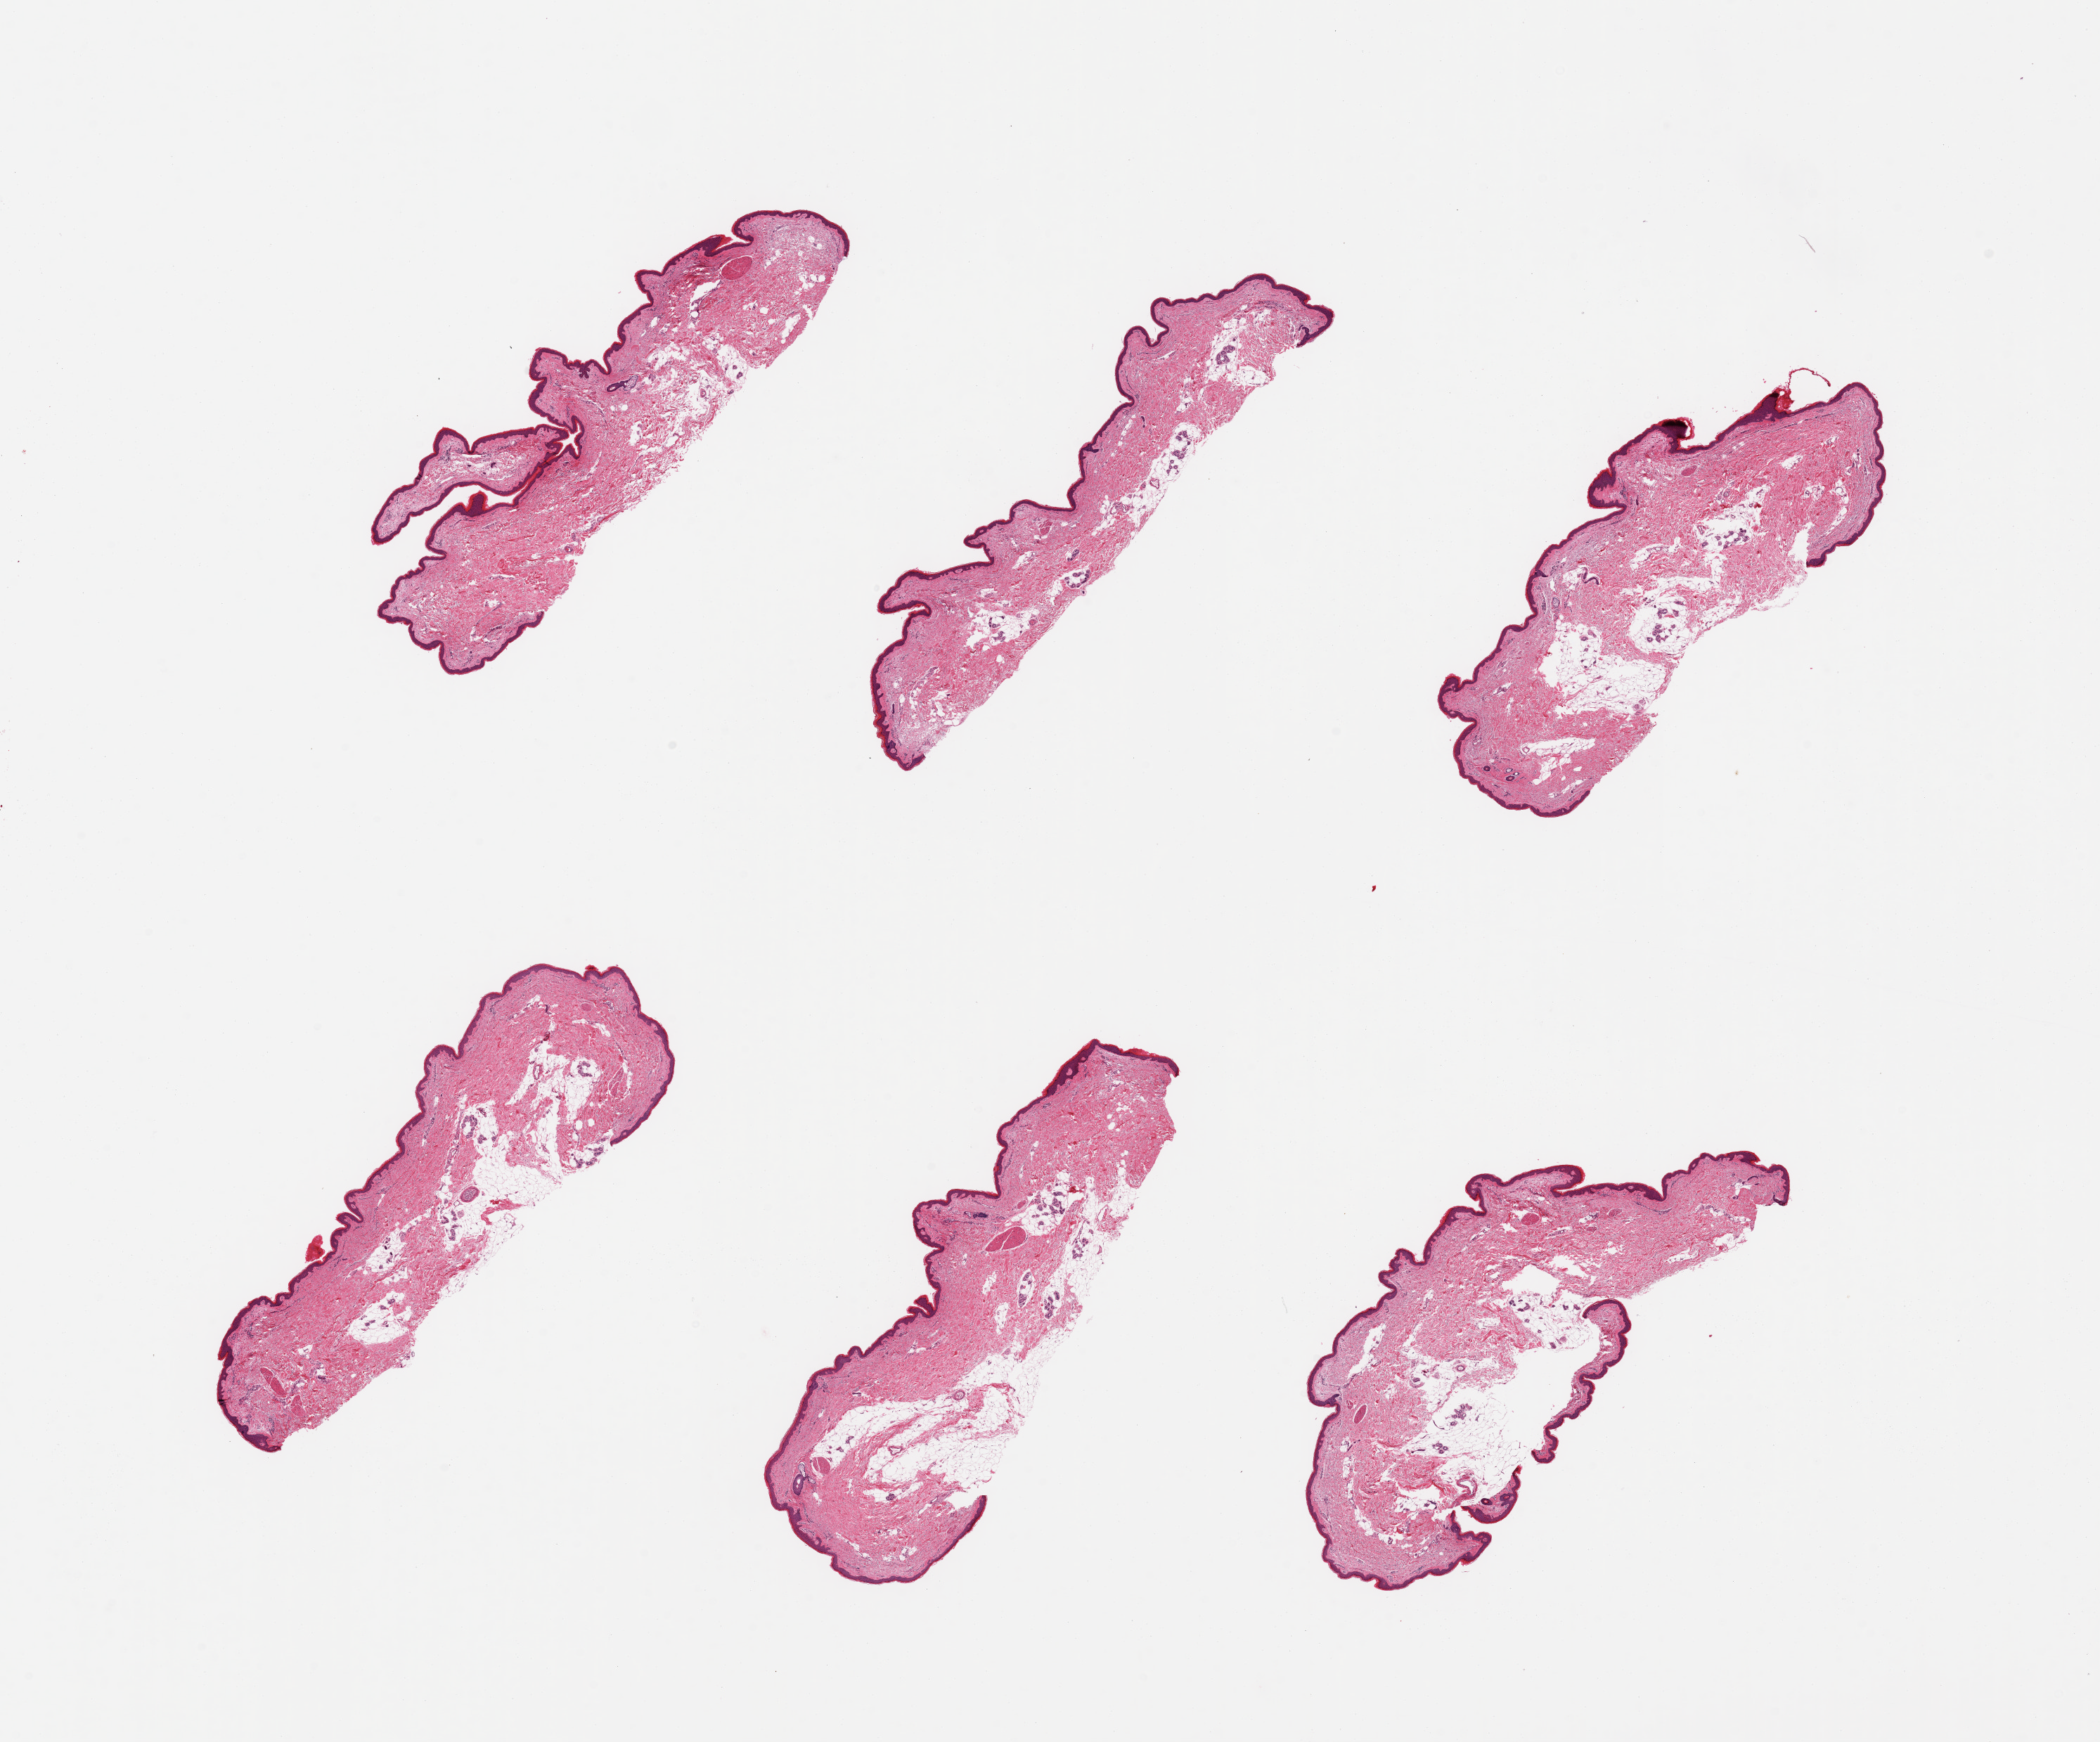
Whole-slide image, hematoxylin and eosin (H&E) stain, brightfield — whole scanned area (about 23.6 x 19.6 mm) shown as a low-resolution overview. PAXgene-fixed, paraffin-embedded tissue. Target tissue: skin of lower leg. Donor tissue sample.
Reviewer comment on this tissue sample: 6 pieces, moderate dermal fat; squamous epithelium is ~35 microns.